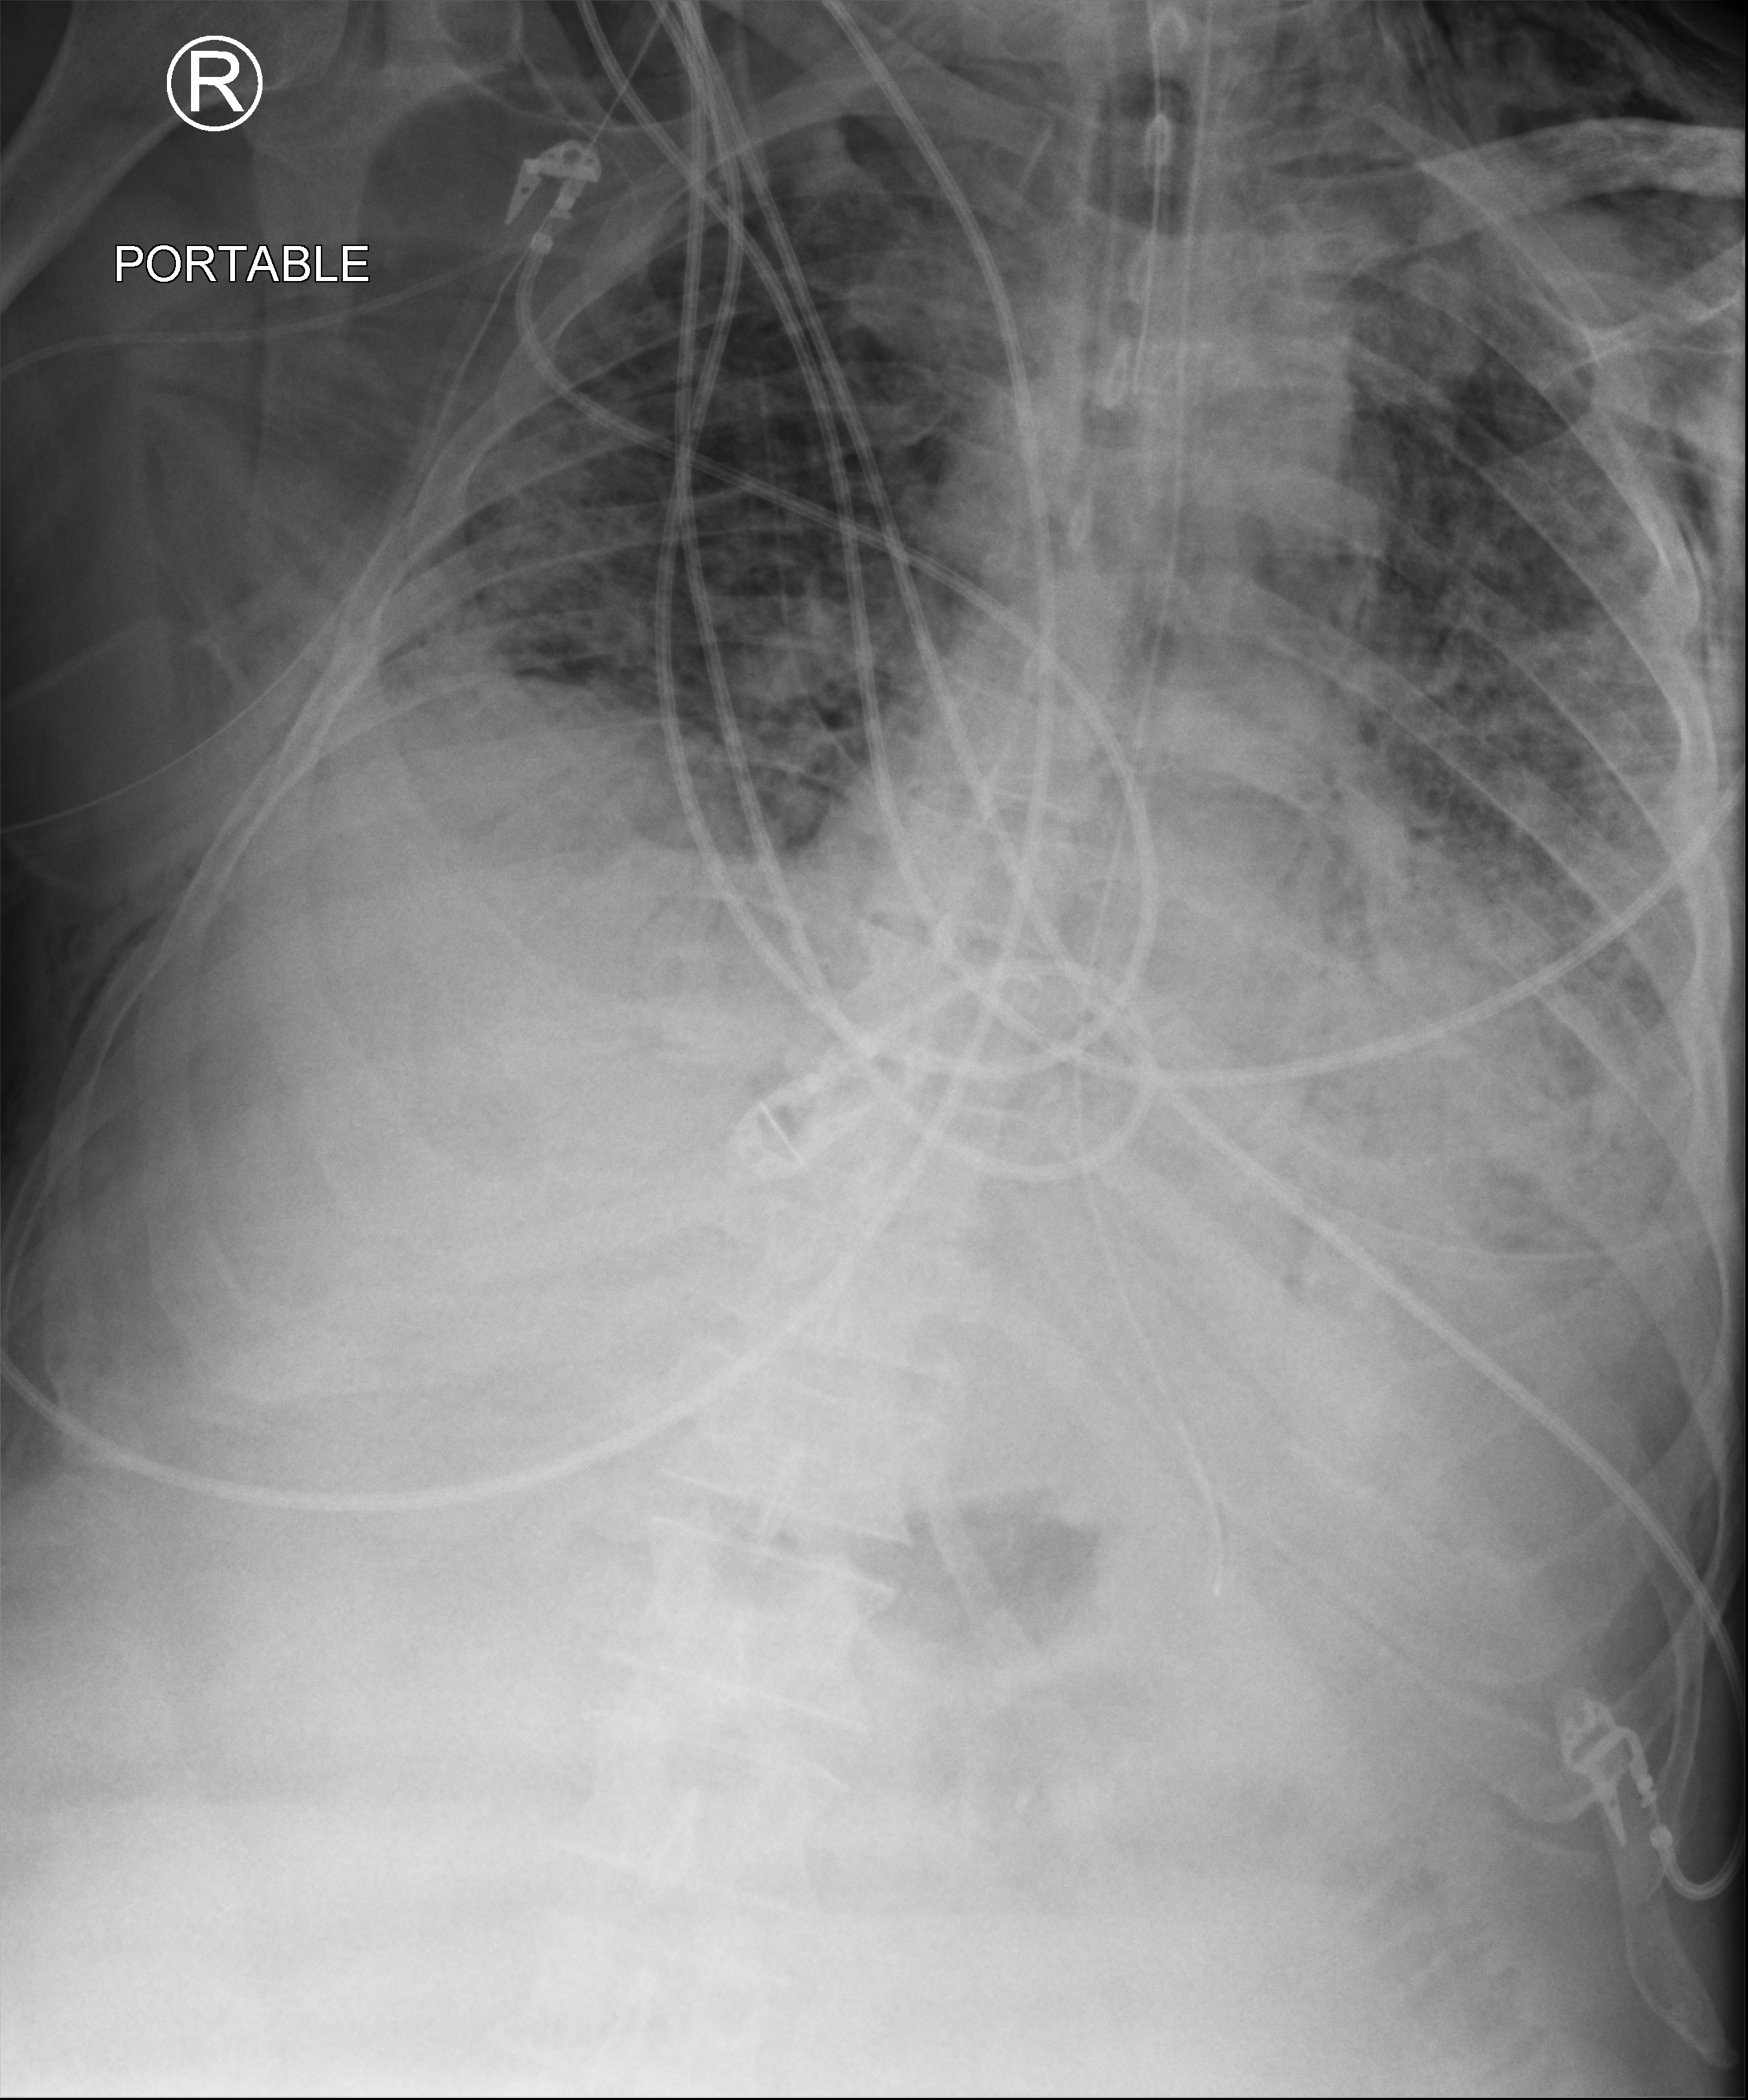
Bedside chest radiograph (computed radiography), anteroposterior (AP) projection. Patient hospitalised with COVID-19; male, aged 60–74 years.
From the hospital-stay record, not from the radiograph (when in the stay this image was taken is not recorded): admitted to intensive care during this hospital stay: yes.